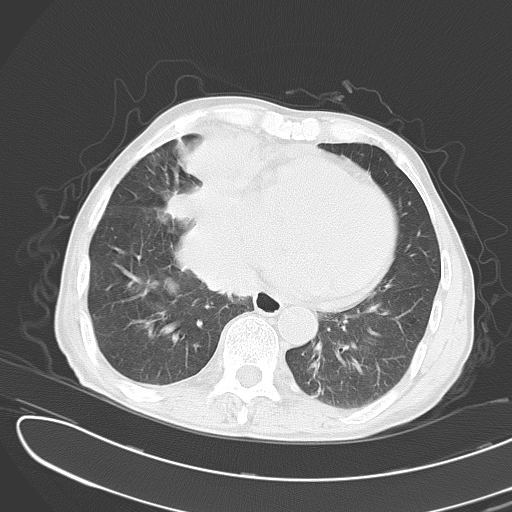
Chest CT, one axial slice. Slice 9 of 43 in the series (ordered by position). Reconstruction kernel B70f. Lung window (W 1500 / L -600 HU). 5 mm slice thickness. 512 × 512 image matrix, field of view 353 × 353 mm. Patient: male, 65 years. From the clinical record (not read from this slice): clinical TNM (as recorded): T2 N3 M1; histopathological grade: G3.
Structures marked on this image (rectangle marked by the reading radiologist):
- lung tumour (recorded histology: small cell carcinoma): bounding box (x1, y1, x2, y2) in pixels: (155, 114, 263, 301)